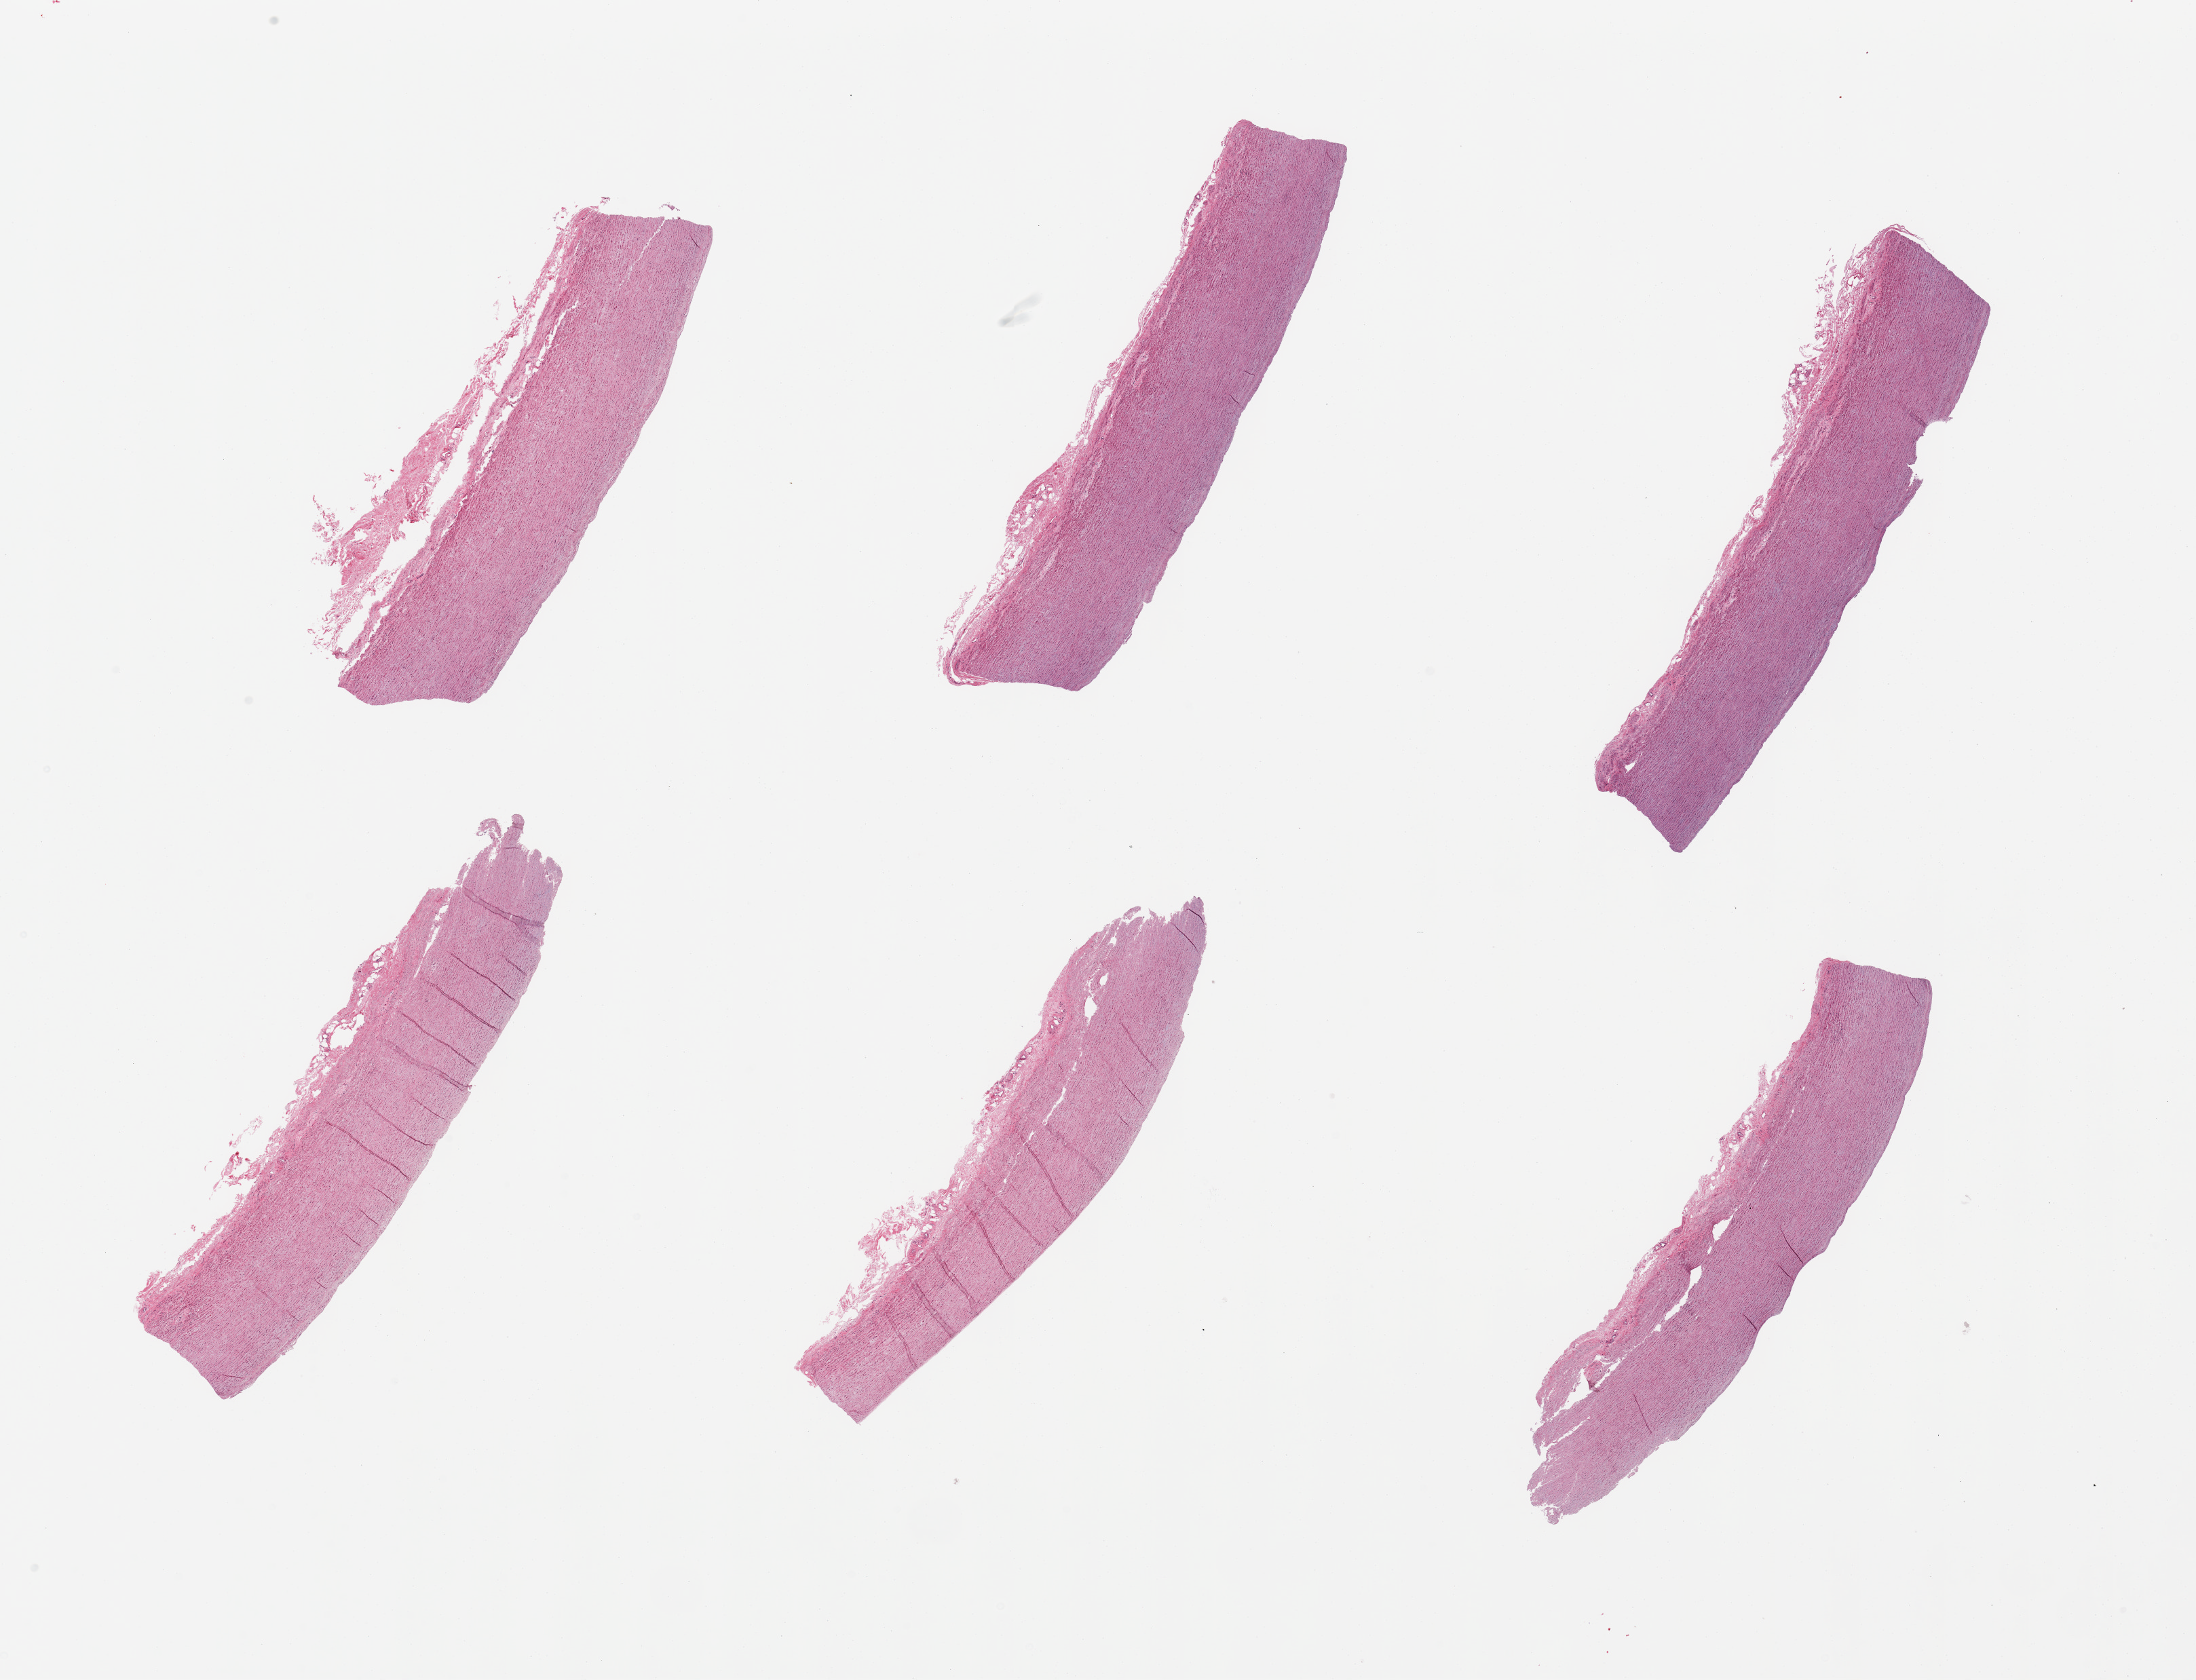
Digitized haematoxylin and eosin-stained section, brightfield, whole scanned area (about 25.6 x 19.6 mm) shown as a low-resolution overview; PAXgene-fixed, paraffin-embedded tissue; sampled site (target tissue): aorta; donor tissue sample. Donor: male.
Review note (as recorded): 6 pieces; sparse rim of adventitia; possible early plaque formation.